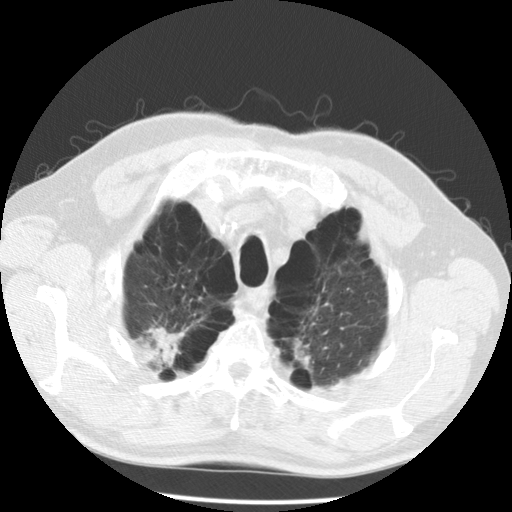
Chest CT (low-dose screening protocol), one axial image, second annual screen, lung window (W 1500 / L -600 HU), 120 kVp, slice 25 of 167 in the series. Male participant, aged 68 years at enrolment. Former smoker at enrolment.
Expert-annotated lung lesion, bounding box <126,303,200,377> (left, top, right, bottom; pixels). The screening reader recorded 2 non-calcified nodules or masses ≥4 mm on this exam (lingula, left lower lobe); which of them this box marks is not recorded. Official screen result: positive, no significant change: stable abnormalities potentially related to lung cancer, unchanged since the prior screening exam. Later outcome: lung cancer diagnosed 617 days after this screen (after the third annual screen) — large cell carcinoma, NOS, right upper lobe, poorly differentiated (G3), stage IV (AJCC 6th edition).